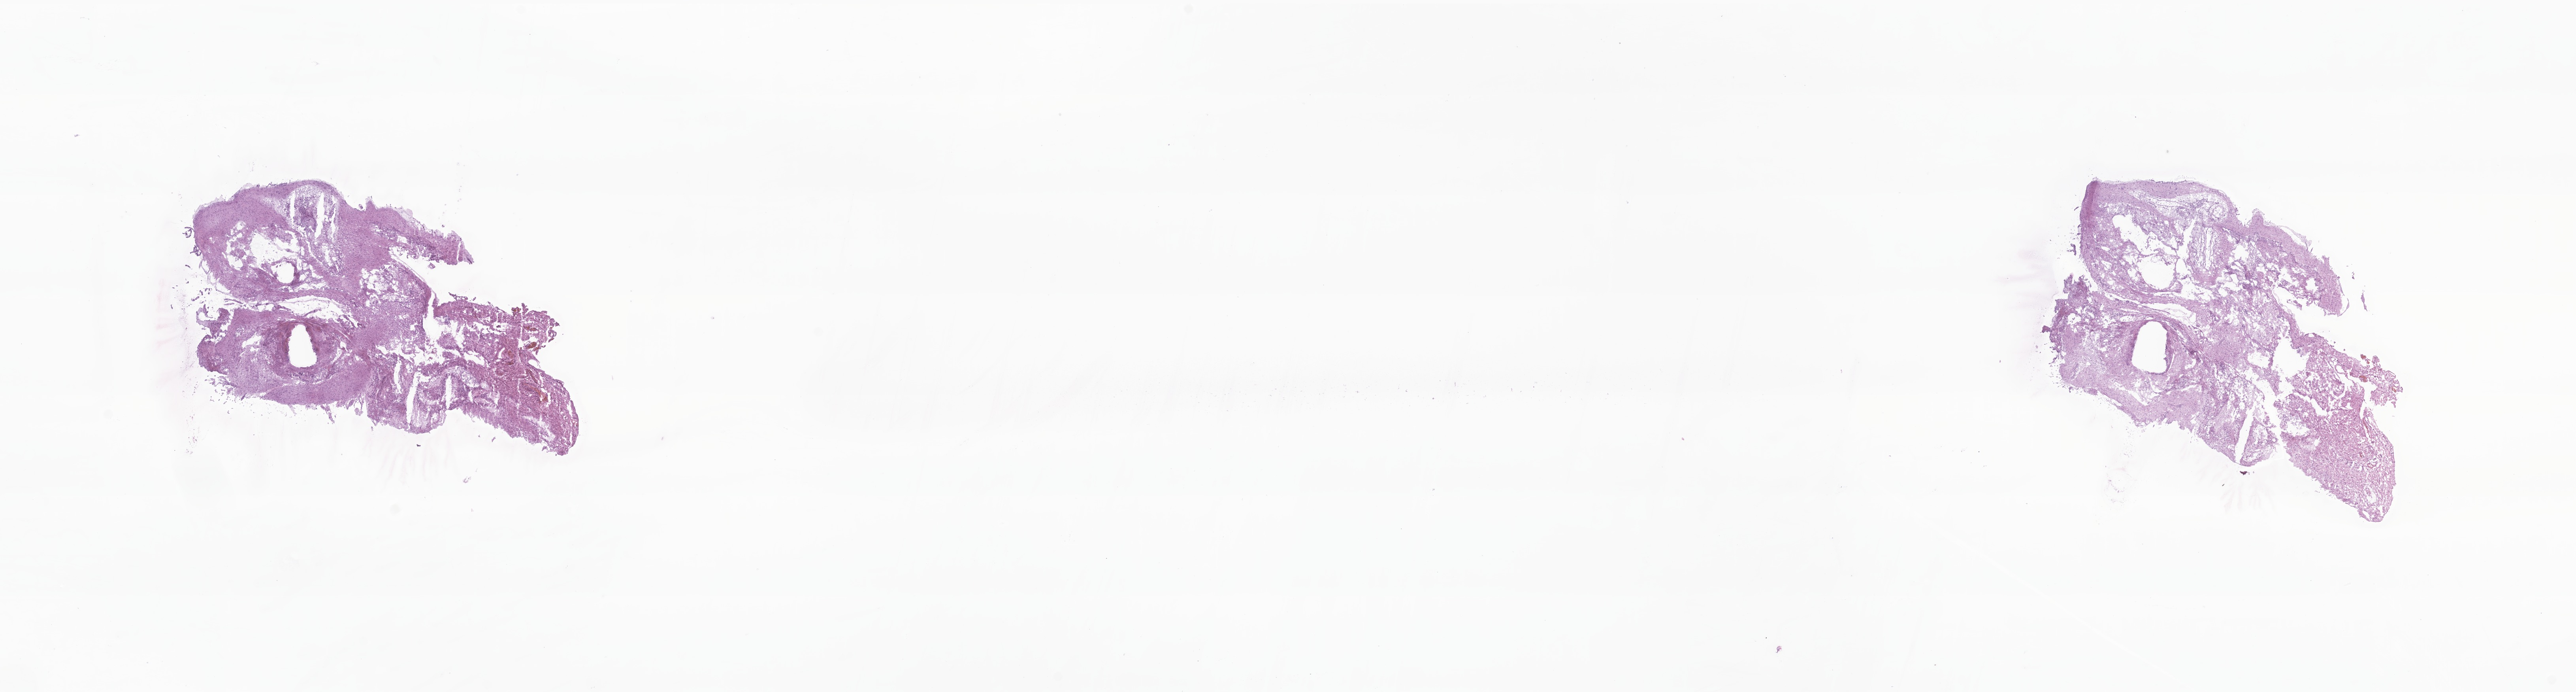
Digitized H&E-stained section of tumor tissue from the brain — shown as a low-resolution overview of the whole scanned area (about 27.5 x 7.4 mm), frozen section. Patient: male, age 64 months (5 years 4 months).
• diagnosis (ICD-O-3 morphology term): Craniopharyngioma, NOS